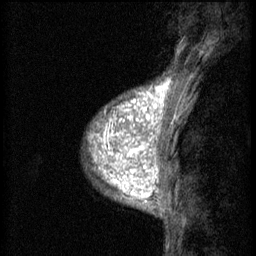
Breast MRI (dynamic contrast-enhanced), one sagittal slice. Slice 15 of 60 in the series (ordered by position). 3 images stored at this slice position (order not interpretable as contrast timing). 1.5 T. TE 4.2 ms, TR 8.2 ms. 2 mm slice thickness. 256 × 256 image matrix. Patient: female, 38 years.
Structures marked on this image (semi-automatic segmentation, software-assisted and operator-edited):
- analysis volume of interest (the breast-tissue region the enhancement analysis was run in; not a lesion): box from (x=92, y=112) to (x=152, y=171) px
- tumour enhancement mask (voxels above the 70 % enhancement threshold inside the analysis volume of interest): (x=92, y=112)–(x=152, y=171)